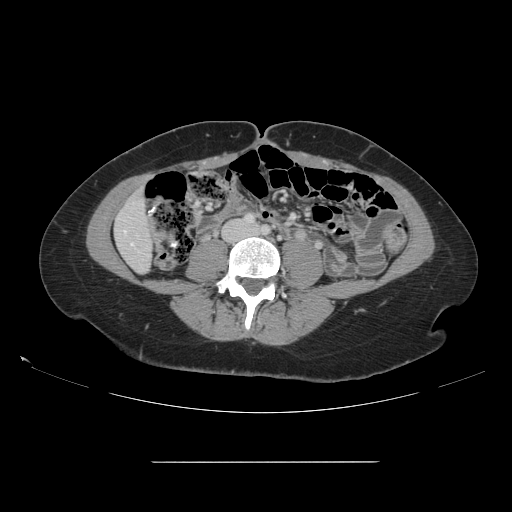
Contrast-enhanced abdominal CT, one axial slice; position 22 of 151 along the scan axis; intravenous contrast given; soft-tissue window (W 400 / L 40 HU); 2.5 mm slice thickness; 512 × 512 image matrix. Female patient, age 46 years. Case-level facts recorded for this patient, not image findings: diagnosis: colorectal cancer liver metastases, imaged before liver resection; multiple liver metastases: yes; largest metastasis: 3 cm; disease in both lobes: yes.
Structures marked on this image (manually delineated by an expert):
- liver: bounding box (x1, y1, x2, y2) in pixels: (116, 191, 152, 272)
- planned liver remnant (the part of the liver to remain after resection): (116, 192, 152, 272)